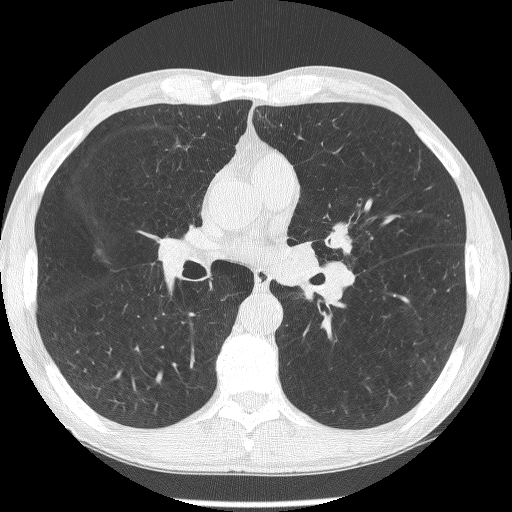
Axial slice from a low-dose chest CT screening exam, second annual screen, lung window (W 1500 / L -600 HU), 512 × 512 image matrix. Male, age 62 years at enrolment. Former smoker at enrolment.
Expert-annotated lung lesion, bounding box <317,217,367,265> (left, top, right, bottom; pixels). The screening reader recorded 2 non-calcified nodules or masses ≥4 mm on this exam (lingula, lingula); which of them this box marks is not recorded.